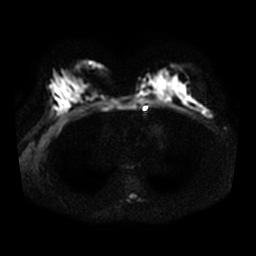
Breast MRI, one axial slice. Slice 19 of 34 in the series (ordered by position). Diffusion-weighted series; image 2 of 4 stored at this slice position (different b-values; order by instance number). 3 T. 5 mm slice thickness. 256 × 256 image matrix, field of view 340 × 340 mm. Female patient.
Annotated regions visible in this slice (manually delineated by an expert):
- tumour on diffusion-weighted imaging: bounding box <203,110,212,118> (left, top, right, bottom; pixels)